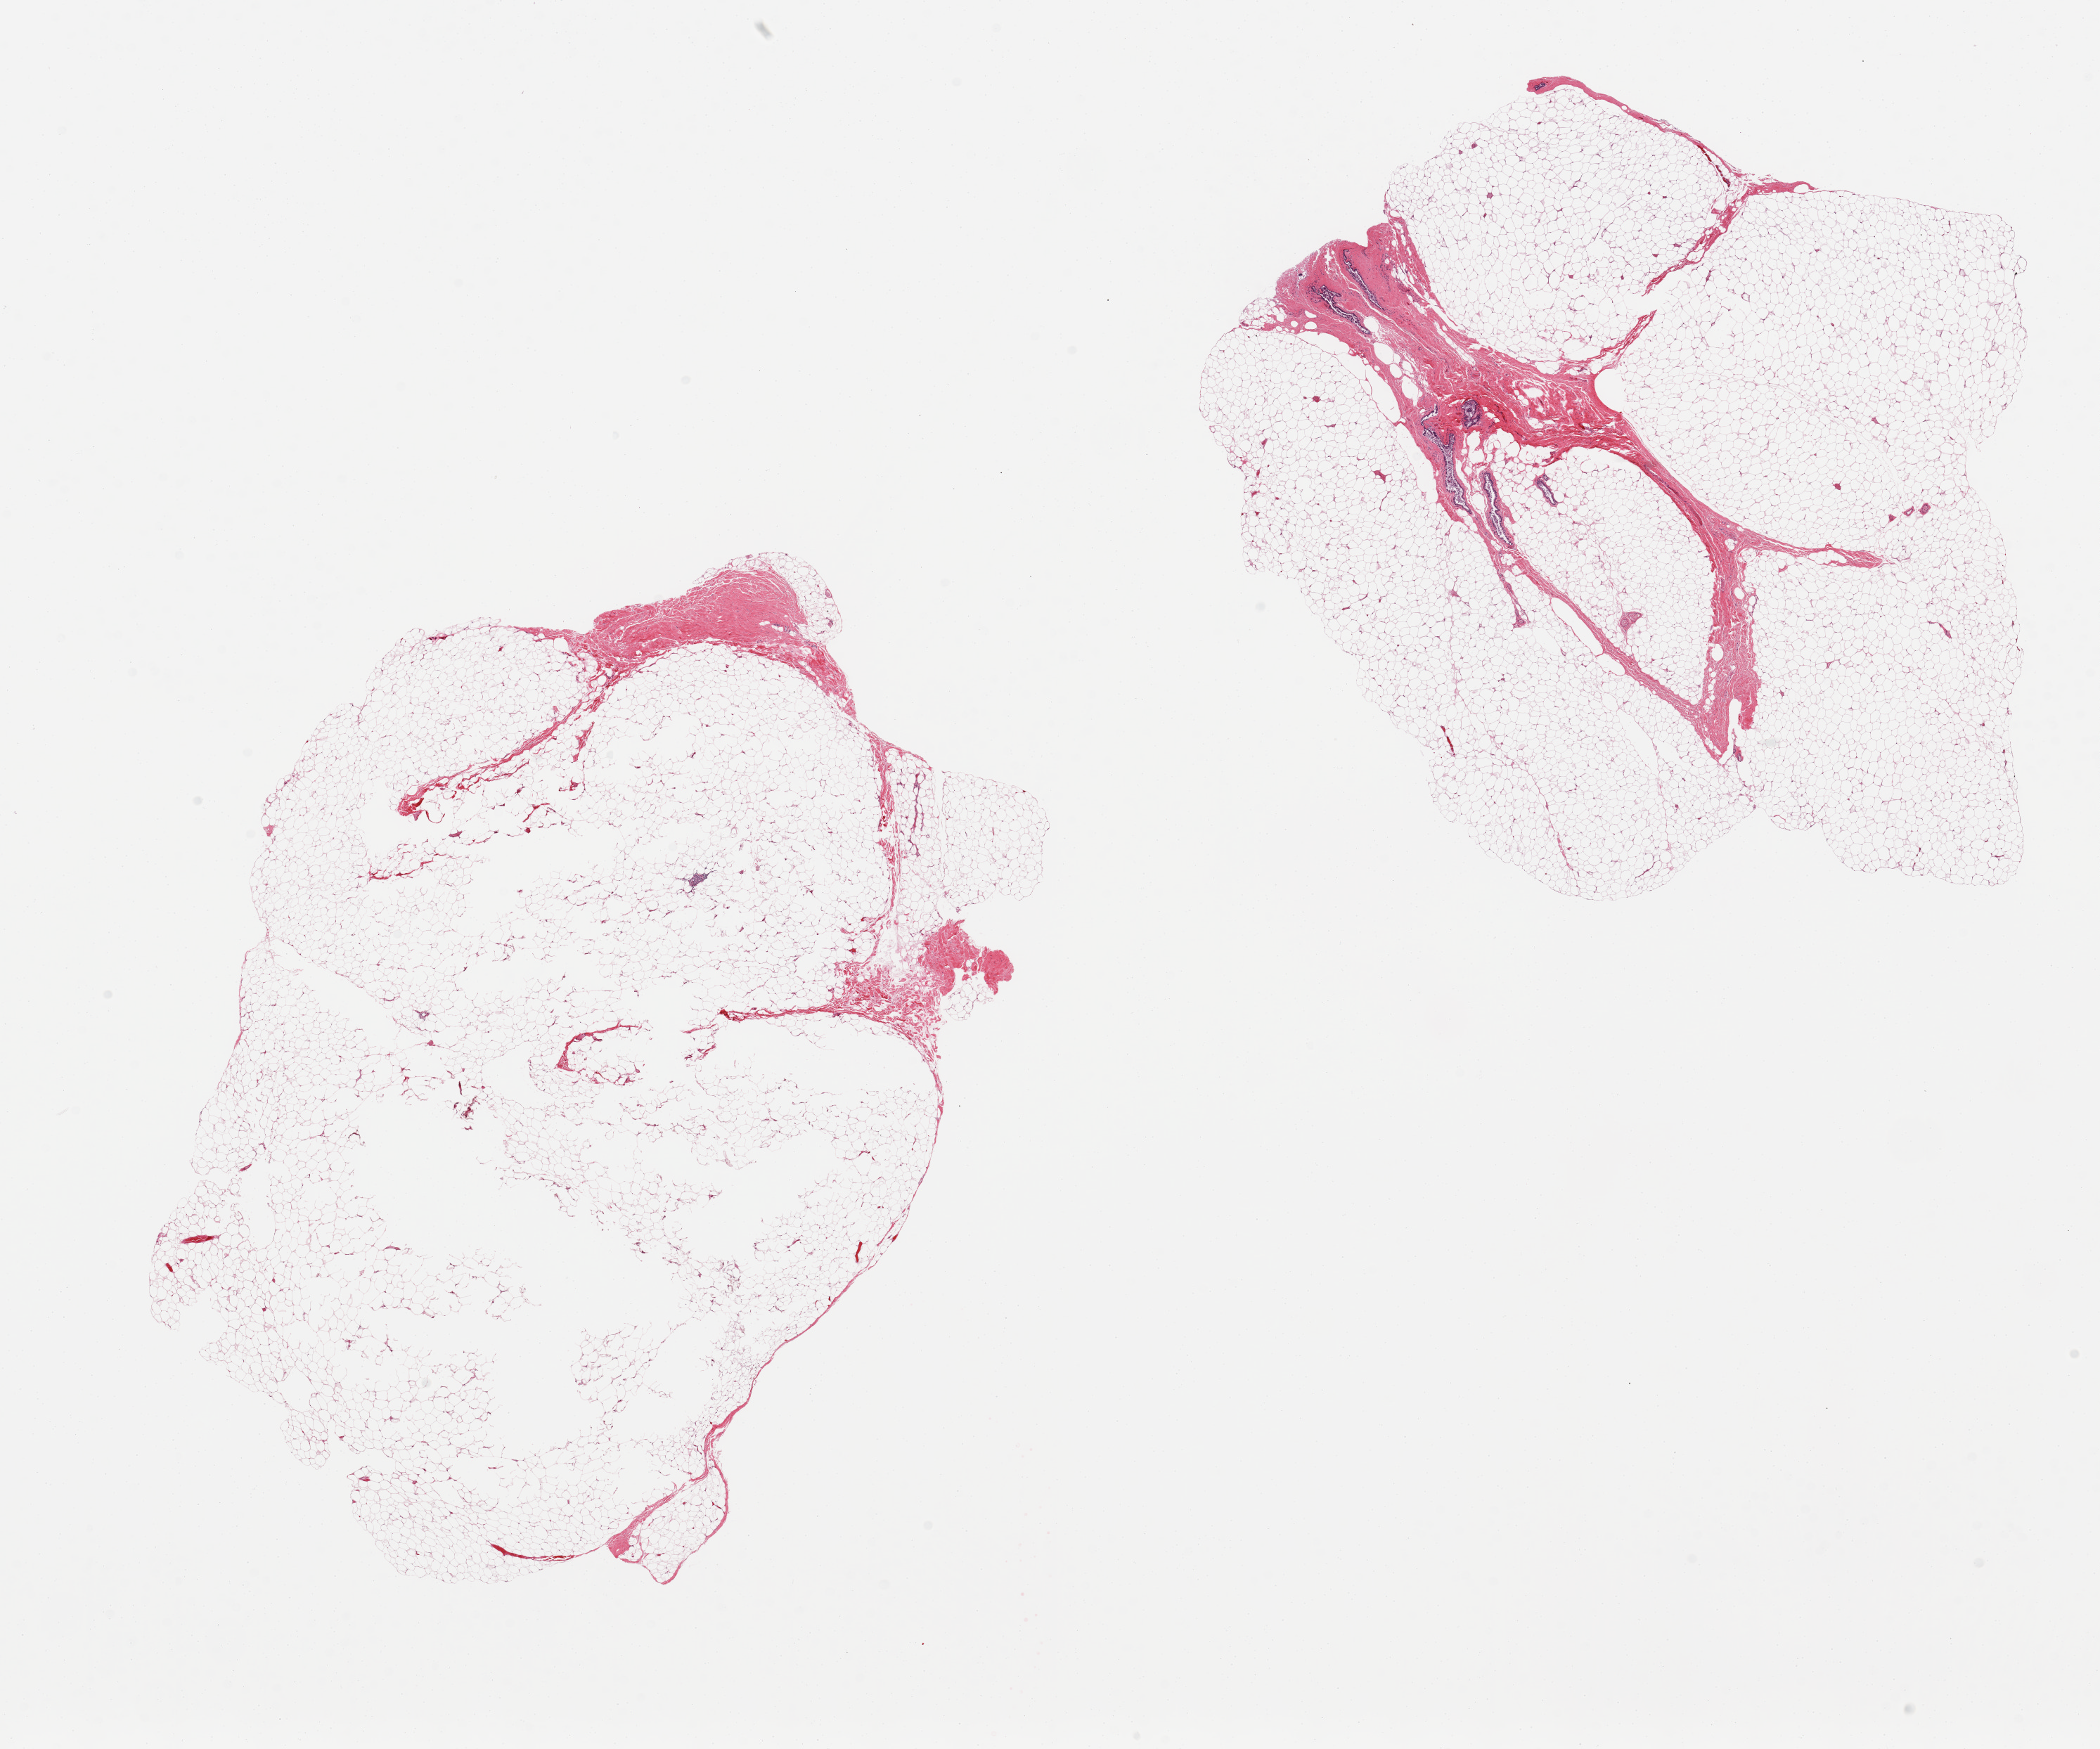
Digitized H&E-stained section — whole scanned area (about 23.6 x 19.7 mm) shown as a low-resolution overview; PAXgene-fixed, paraffin-embedded tissue; sampled site (target tissue): breast; donor tissue sample. Donor sex: male.
Reviewer comment on this tissue sample: 2 pieces, one piece is fat with scant fibrous stroma and few central holes, second includes ~10% fibrous stroma with few ducts, epithelium sloughed.